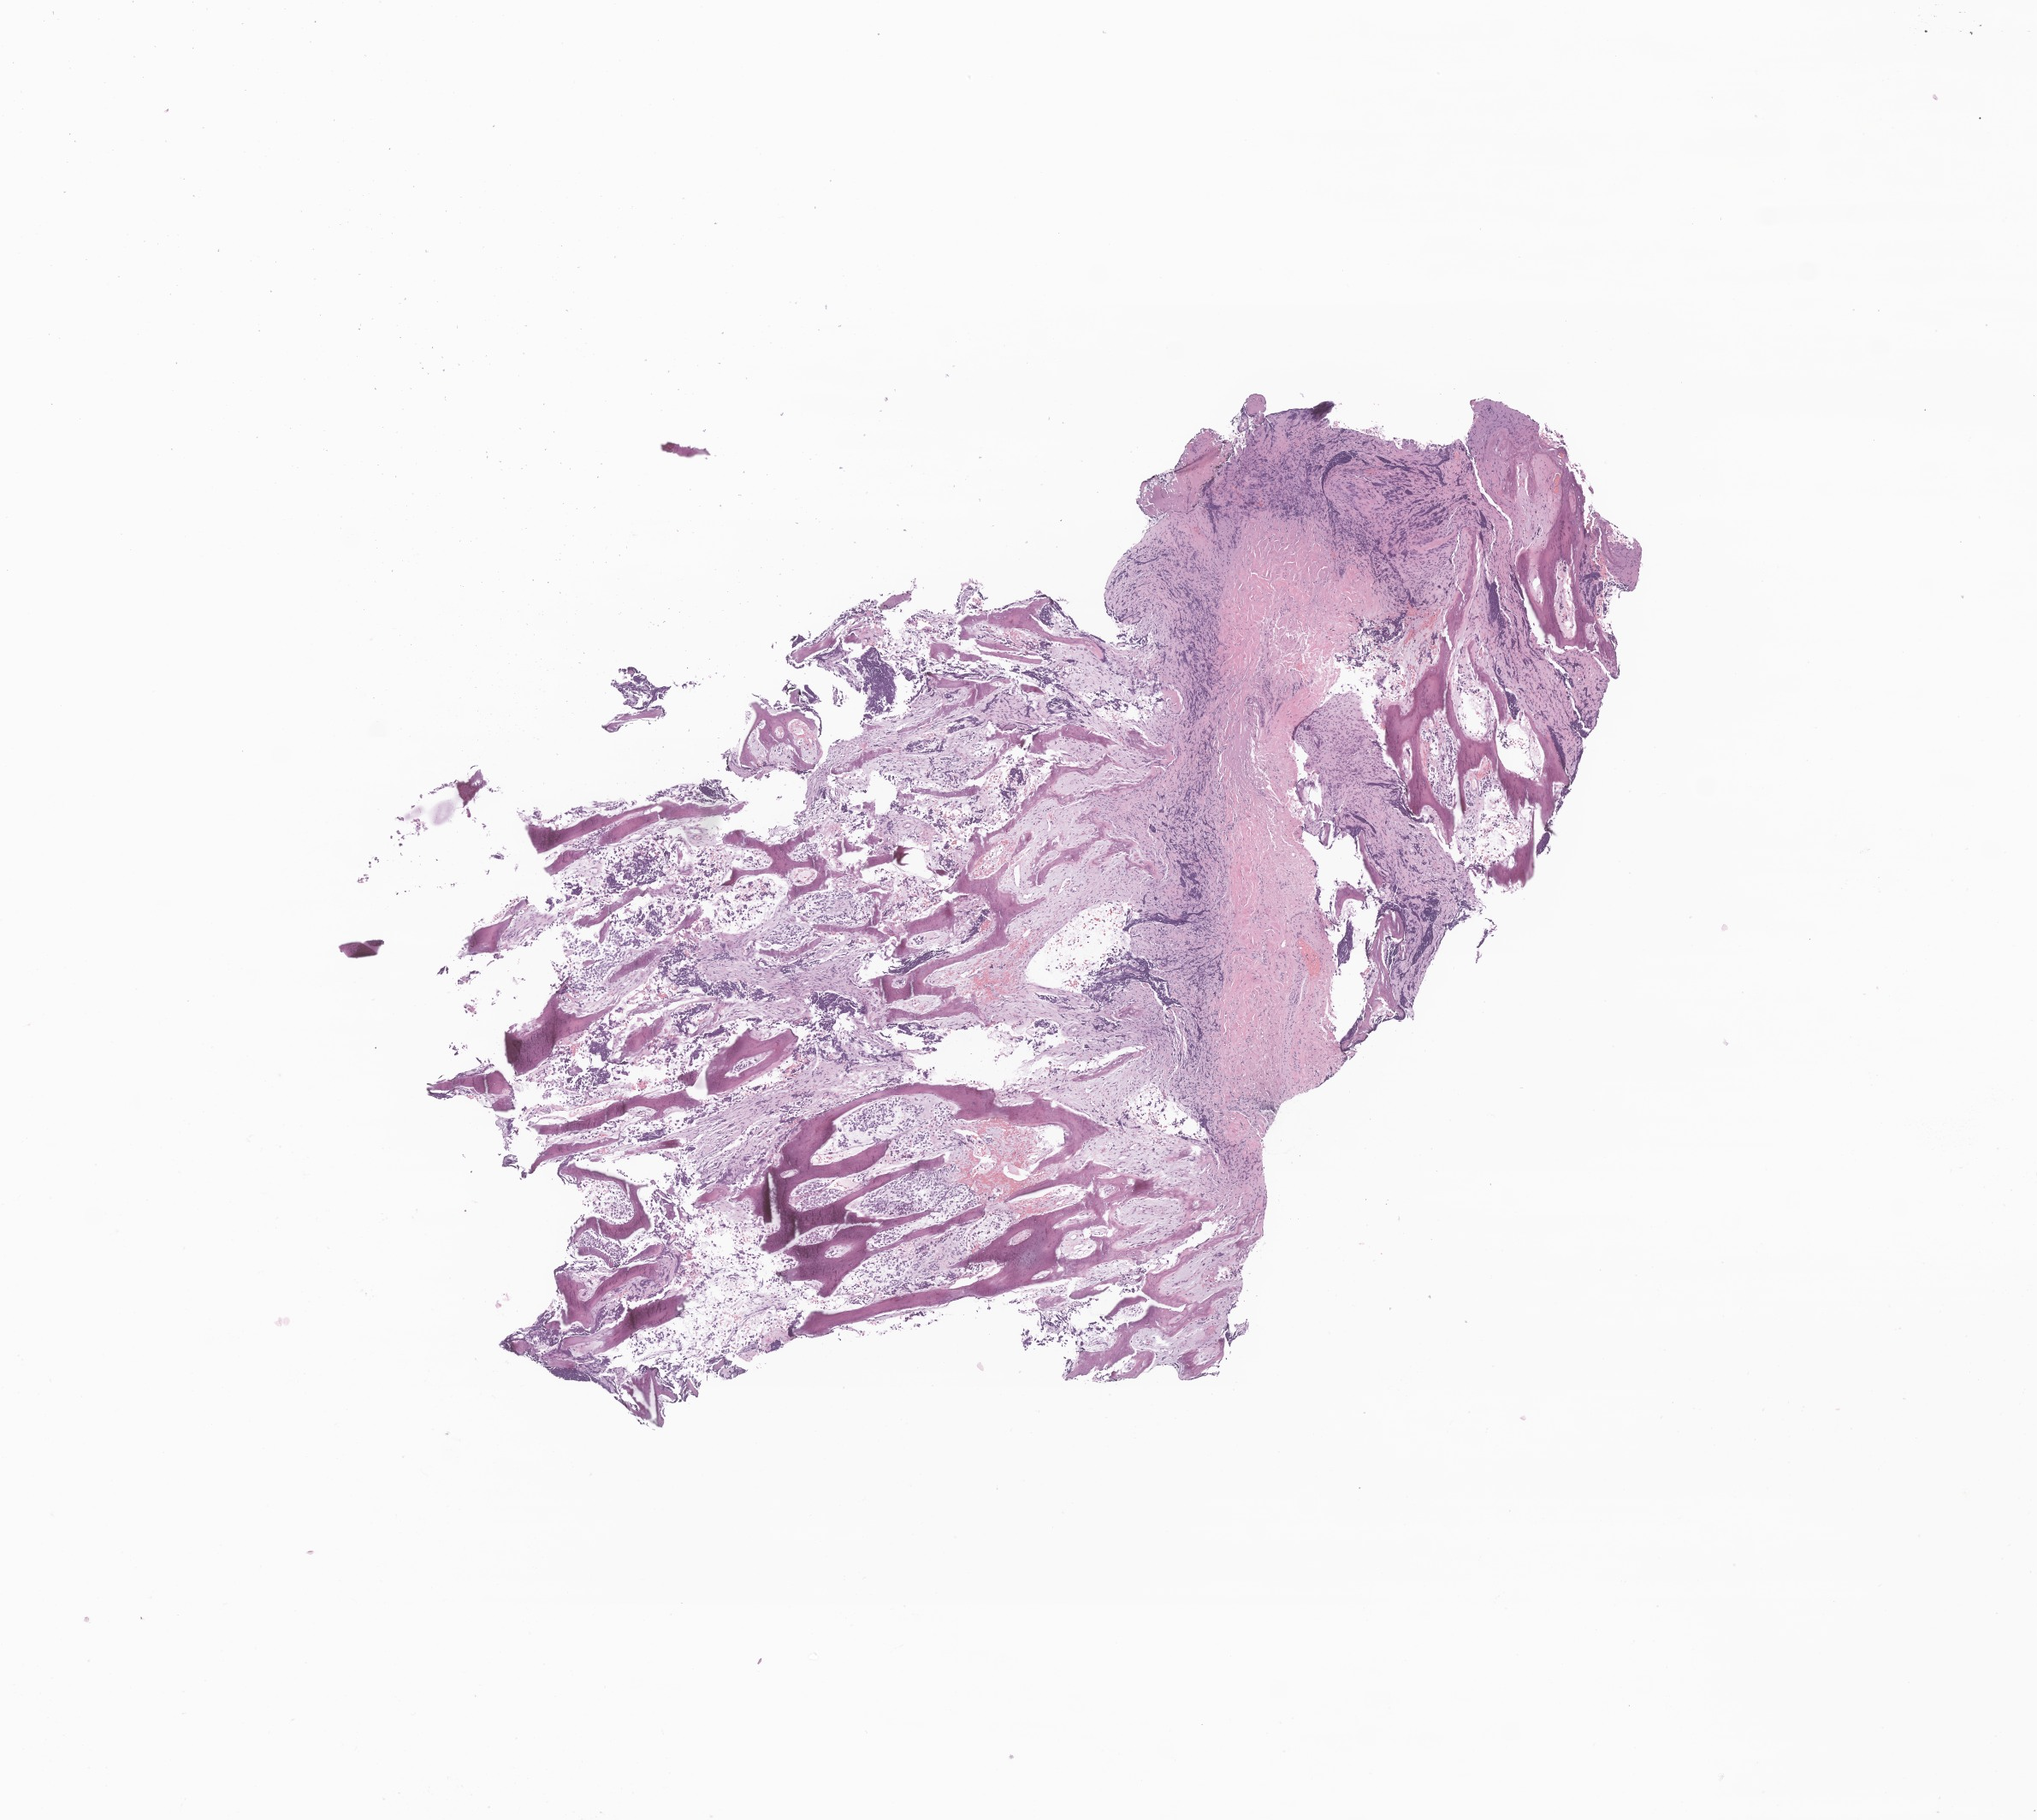
Digitized haematoxylin and eosin-stained section of tumor tissue from the adrenal gland — whole scanned area (about 10.0 x 9.0 mm) shown as a low-resolution overview. Formalin-fixed paraffin-embedded section. Patient: female, age 688 days (about 1.9 years).
Recorded diagnosis: Neuroblastoma, NOS.